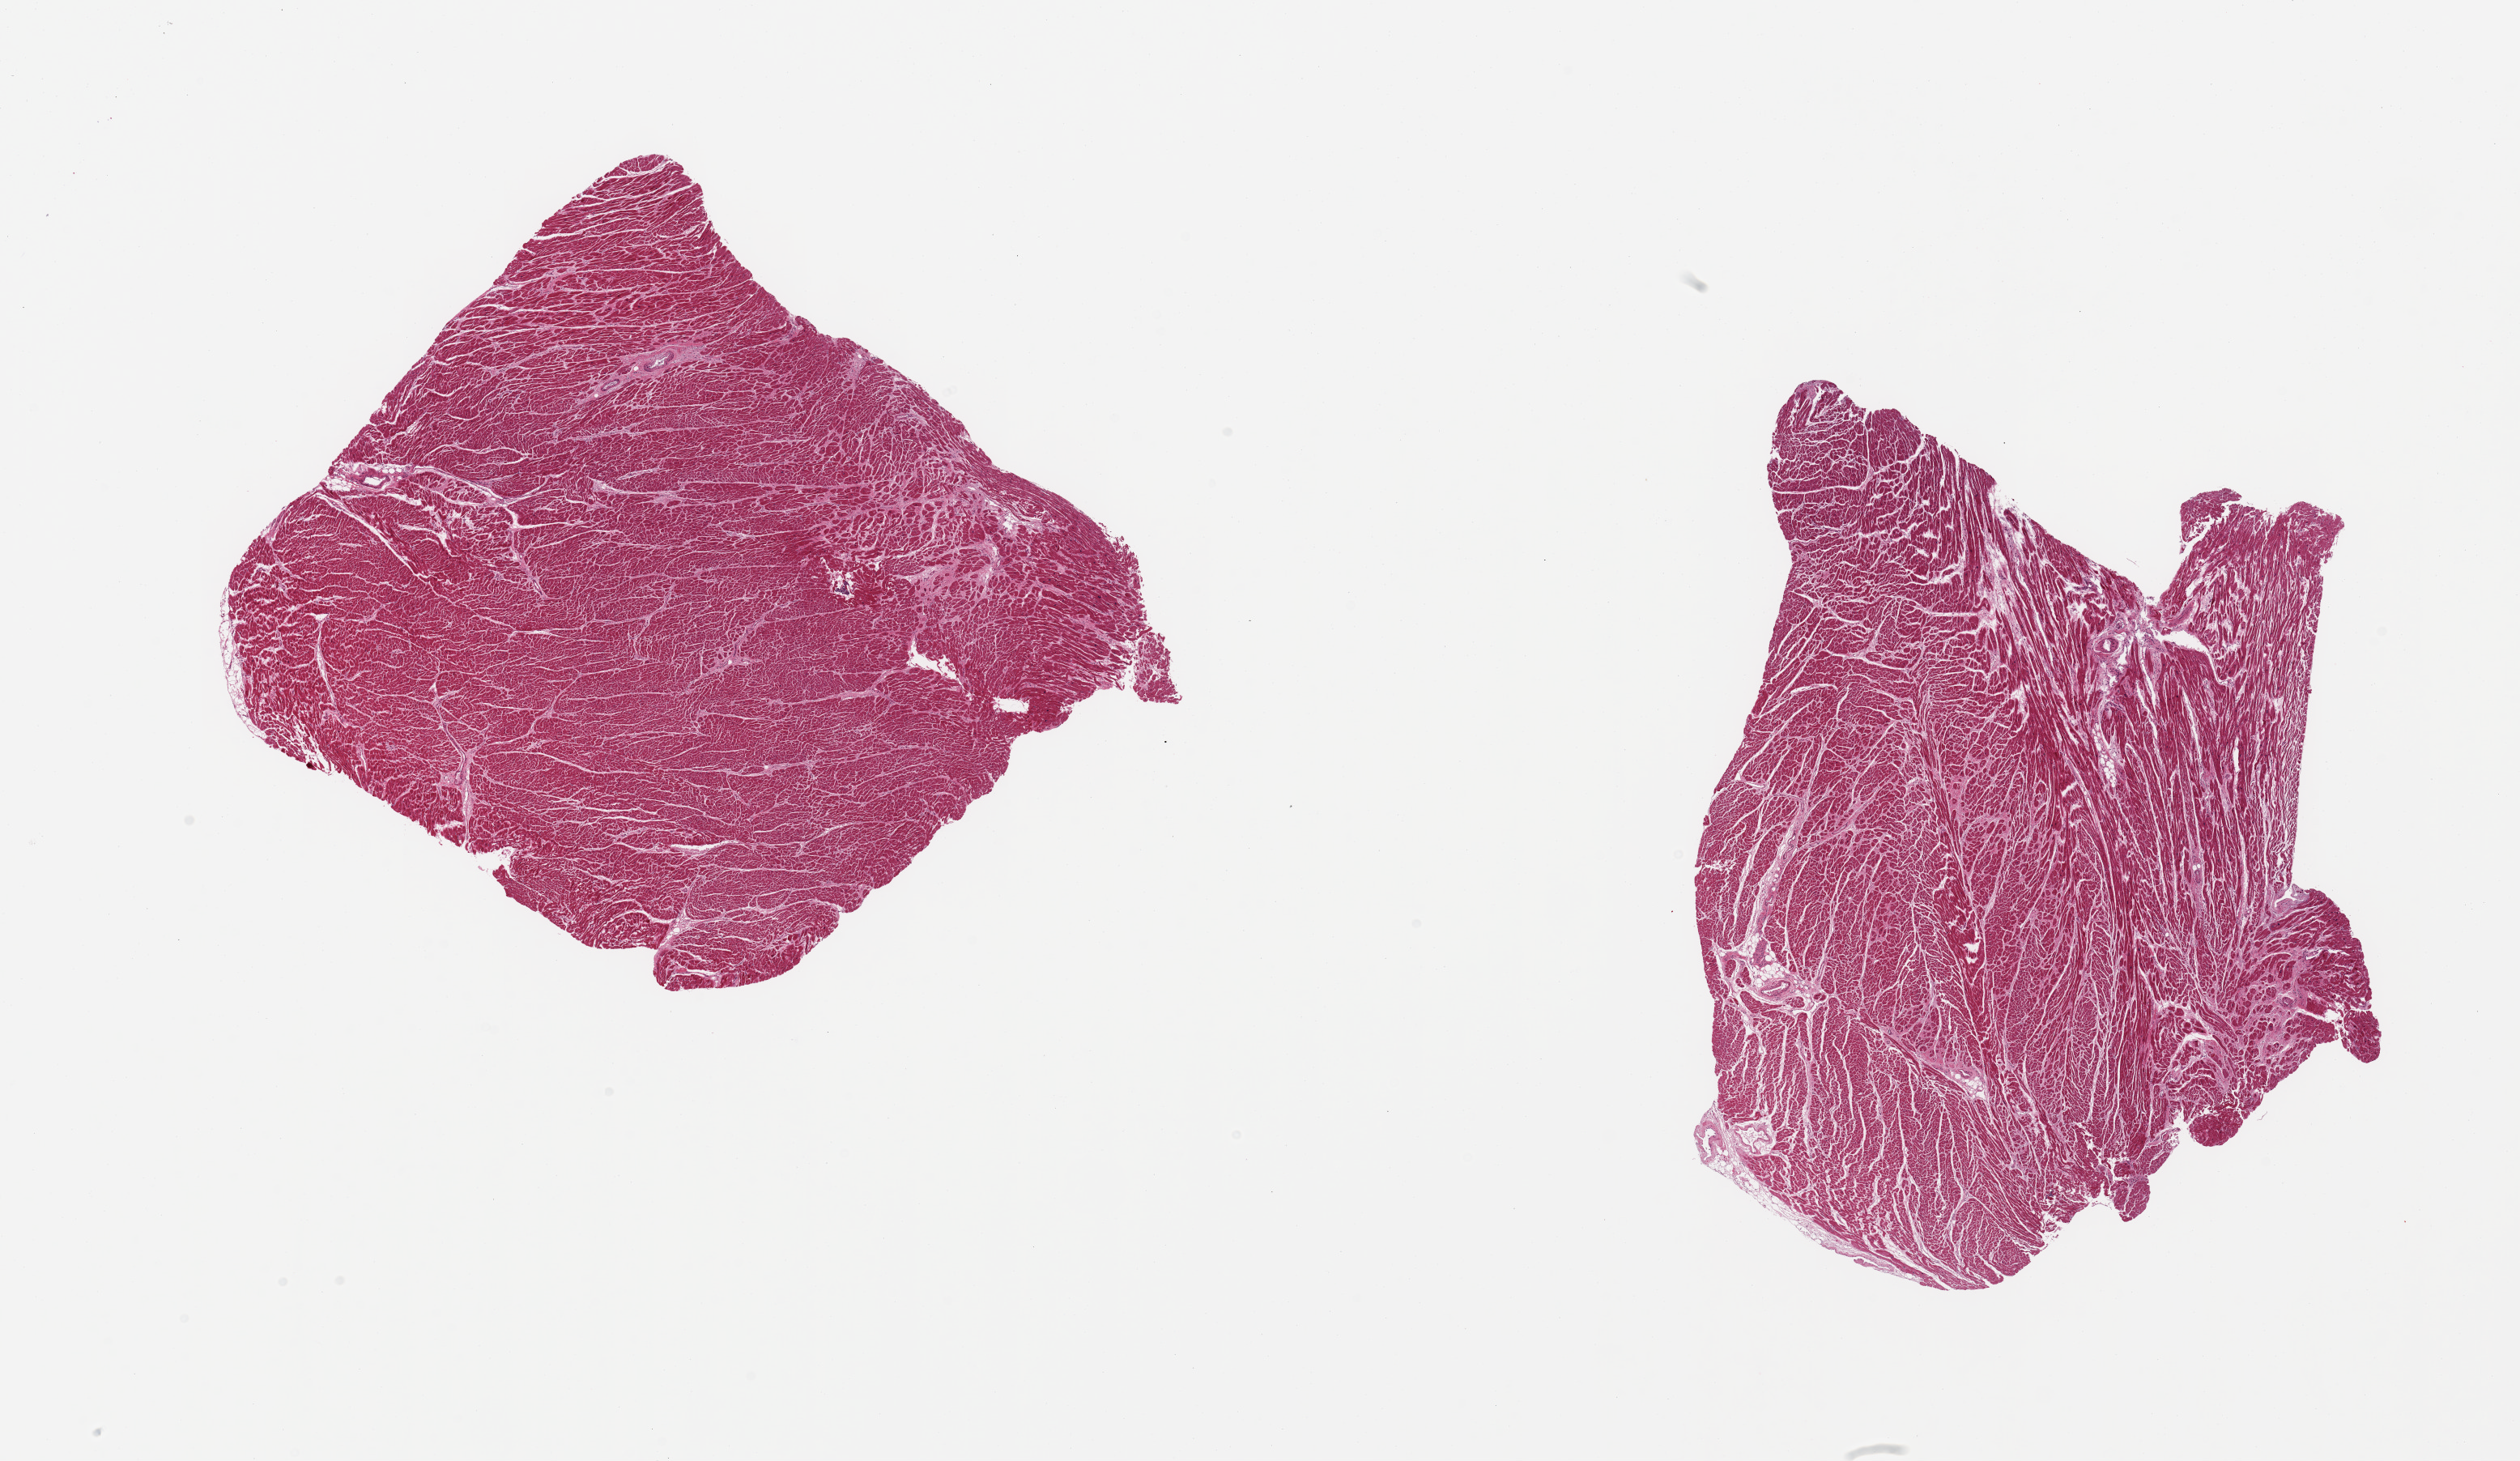
Whole-slide image, hematoxylin and eosin (H&E) stain — low-resolution overview of the scanned area, about 24.6 x 14.3 mm (slide scanned at 20x); PAXgene-fixed, paraffin-embedded tissue; section of heart (target tissue); donor tissue sample. Donor sex: male.
• review note (as recorded): 2 pieces